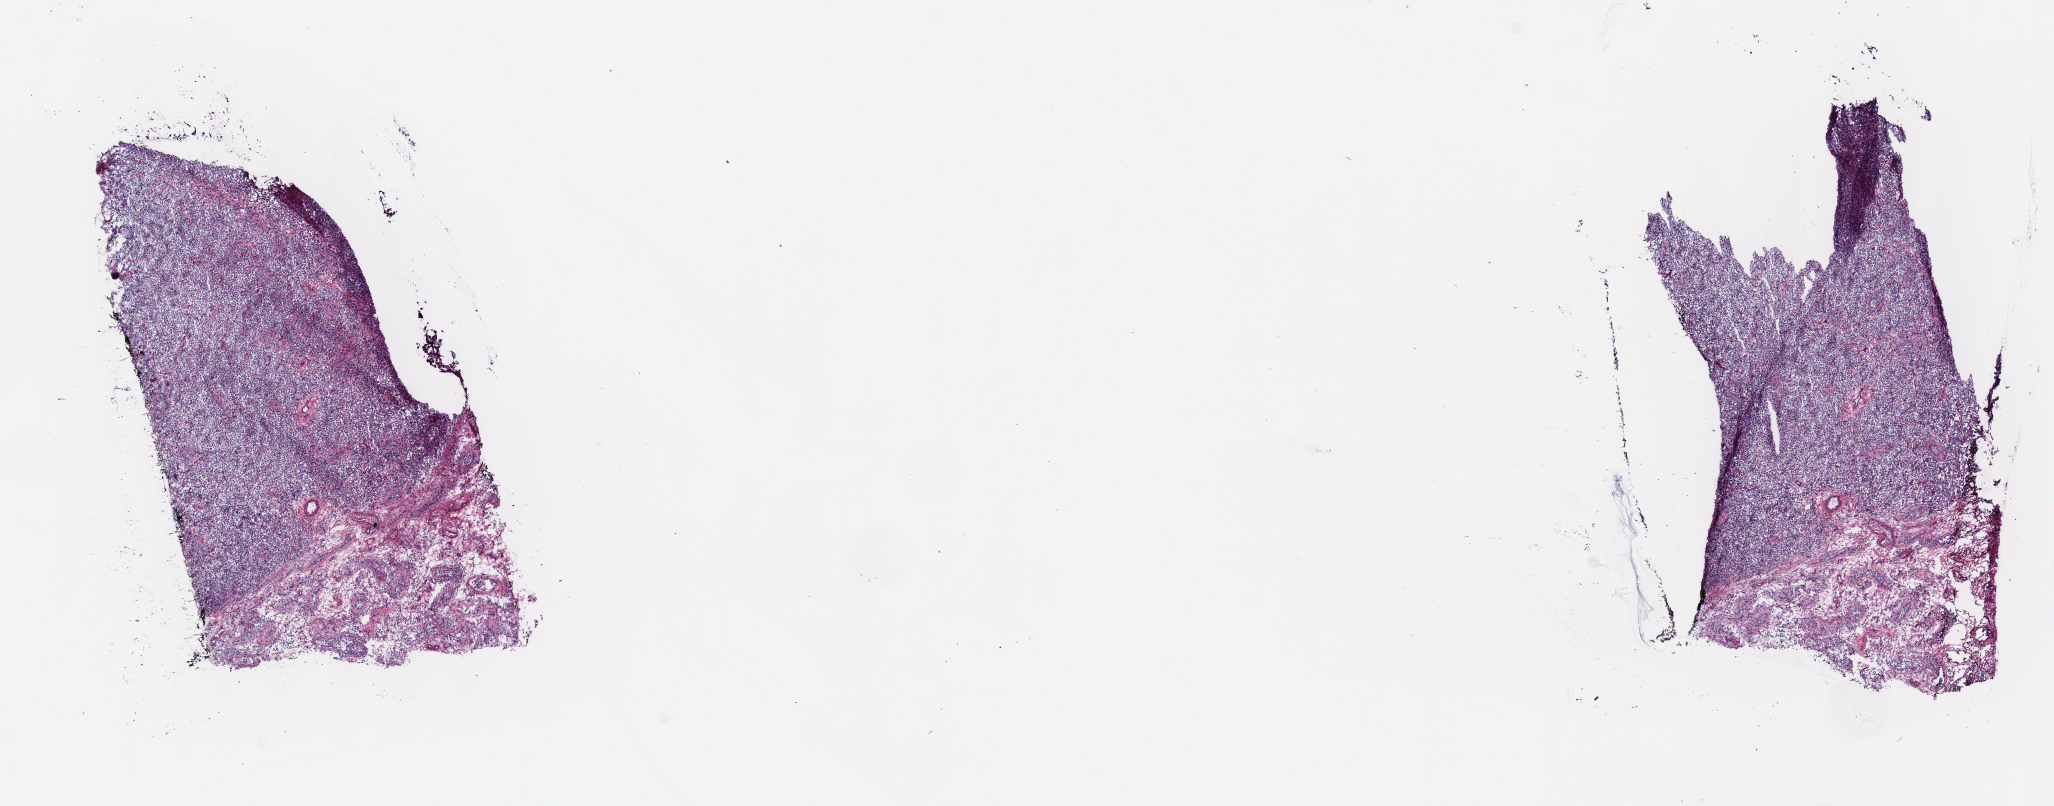
H&E whole-slide image, whole scanned area (about 16.6 x 6.5 mm) shown as a low-resolution overview, frozen section, primary tumour sample from the testis. Male, age 28 years at initial diagnosis. Composition of this section per pathologist review: tumour cells 75%, tumour nuclei 85%, normal cells 25%, stromal cells 0%, necrosis 0%. Infiltration values recorded for this section: lymphocyte infiltration 0%, monocyte infiltration 0%, neutrophil infiltration 0%.
TNM: T1 NX. Histologic diagnosis: Seminoma, NOS. AJCC pathologic stage: I (7th edition).